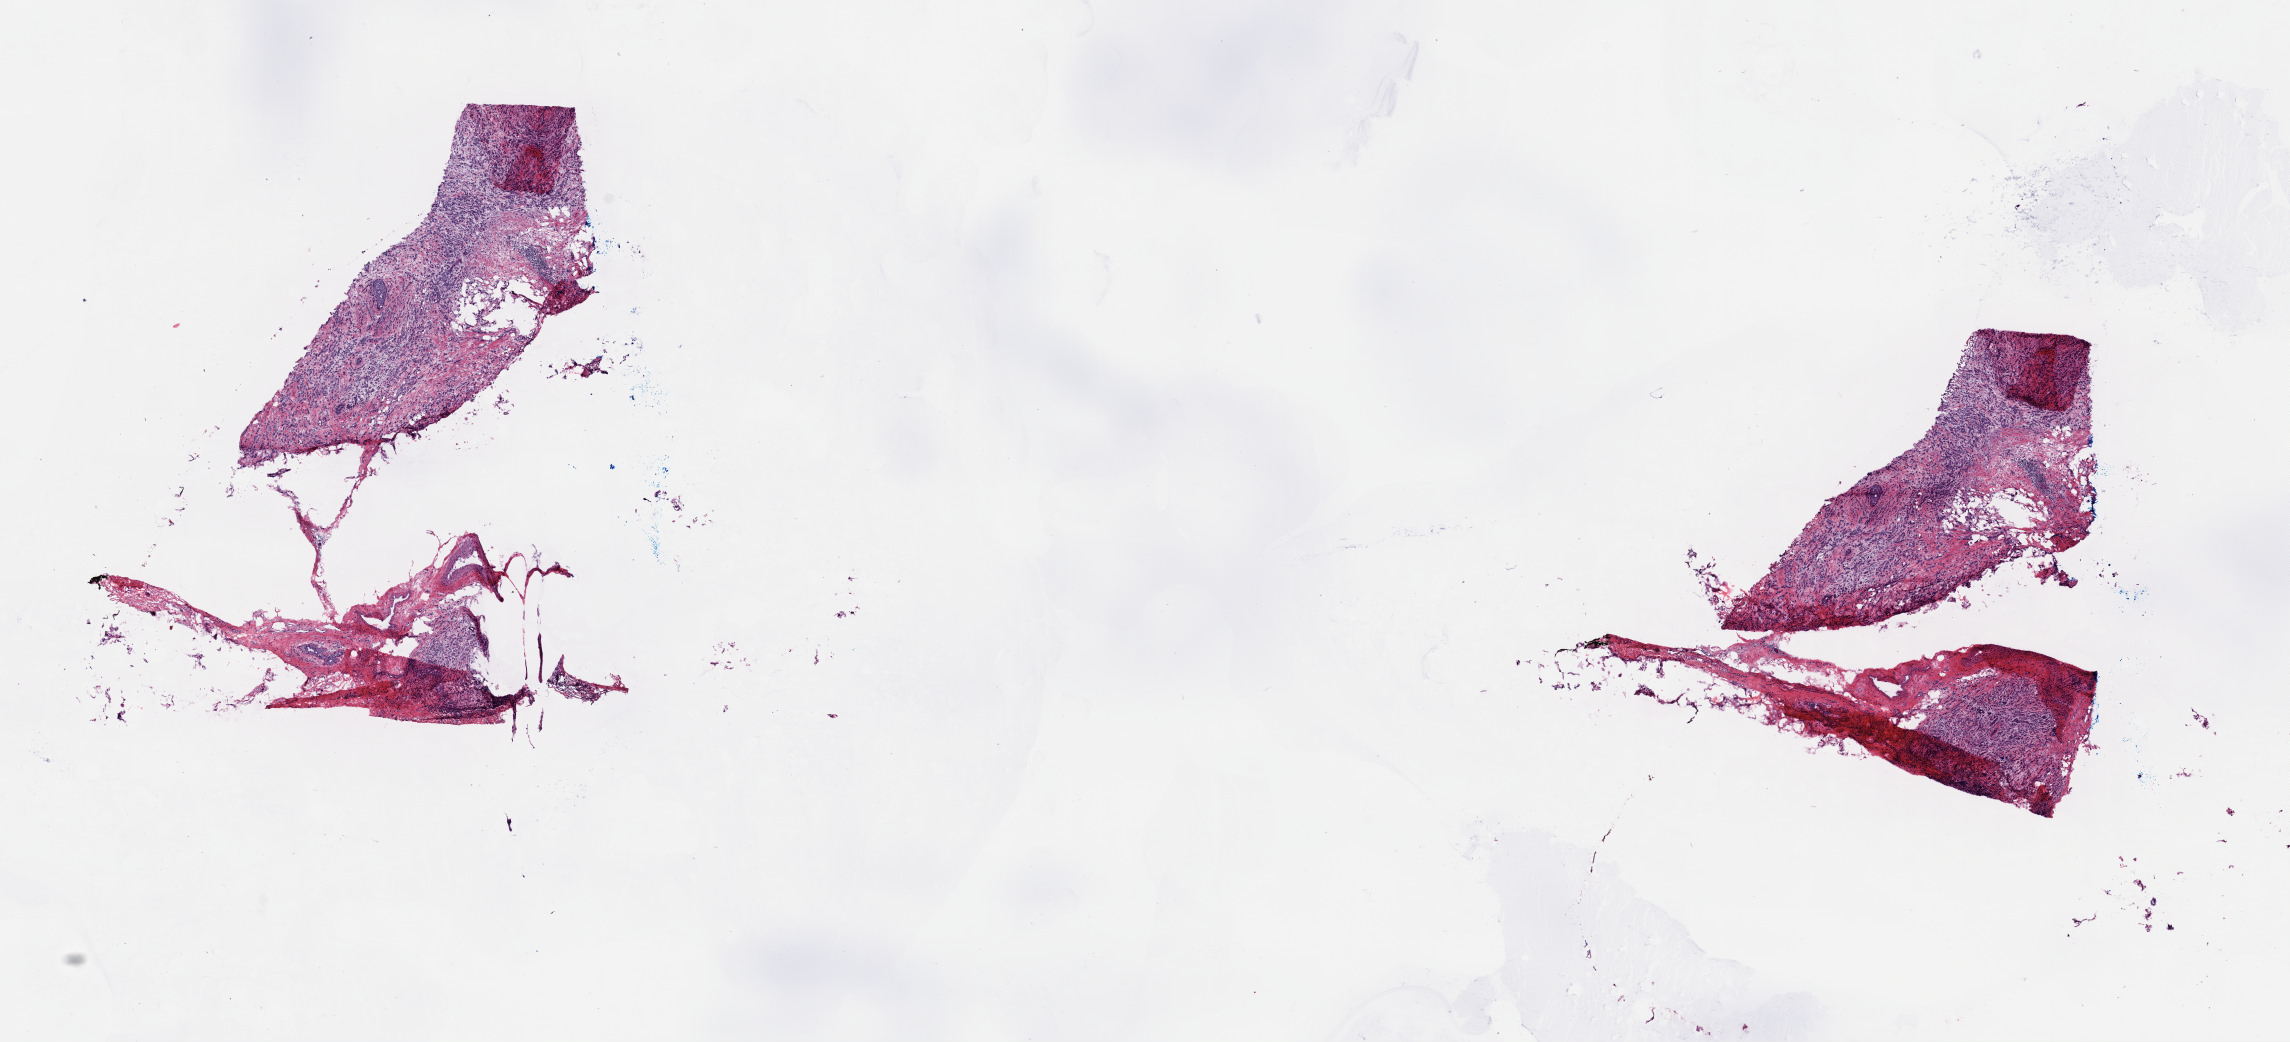
H&E-stained whole-slide image — low-resolution overview of the scanned area, about 18.1 x 8.2 mm. Frozen section. Primary tumour sample from the breast. Female patient; age at initial diagnosis 40 years. Pathologist review of this section (percent, as recorded): tumour cells 60%, tumour nuclei 80%, normal cells 3%, stromal cells 37%, necrosis 0%. Inflammatory infiltration, as recorded: lymphocyte infiltration 2%, monocyte infiltration 0%, neutrophil infiltration 0%.
- laterality: right
- diagnosis: Lobular carcinoma, NOS
- AJCC pathologic stage: IIB (6th edition)